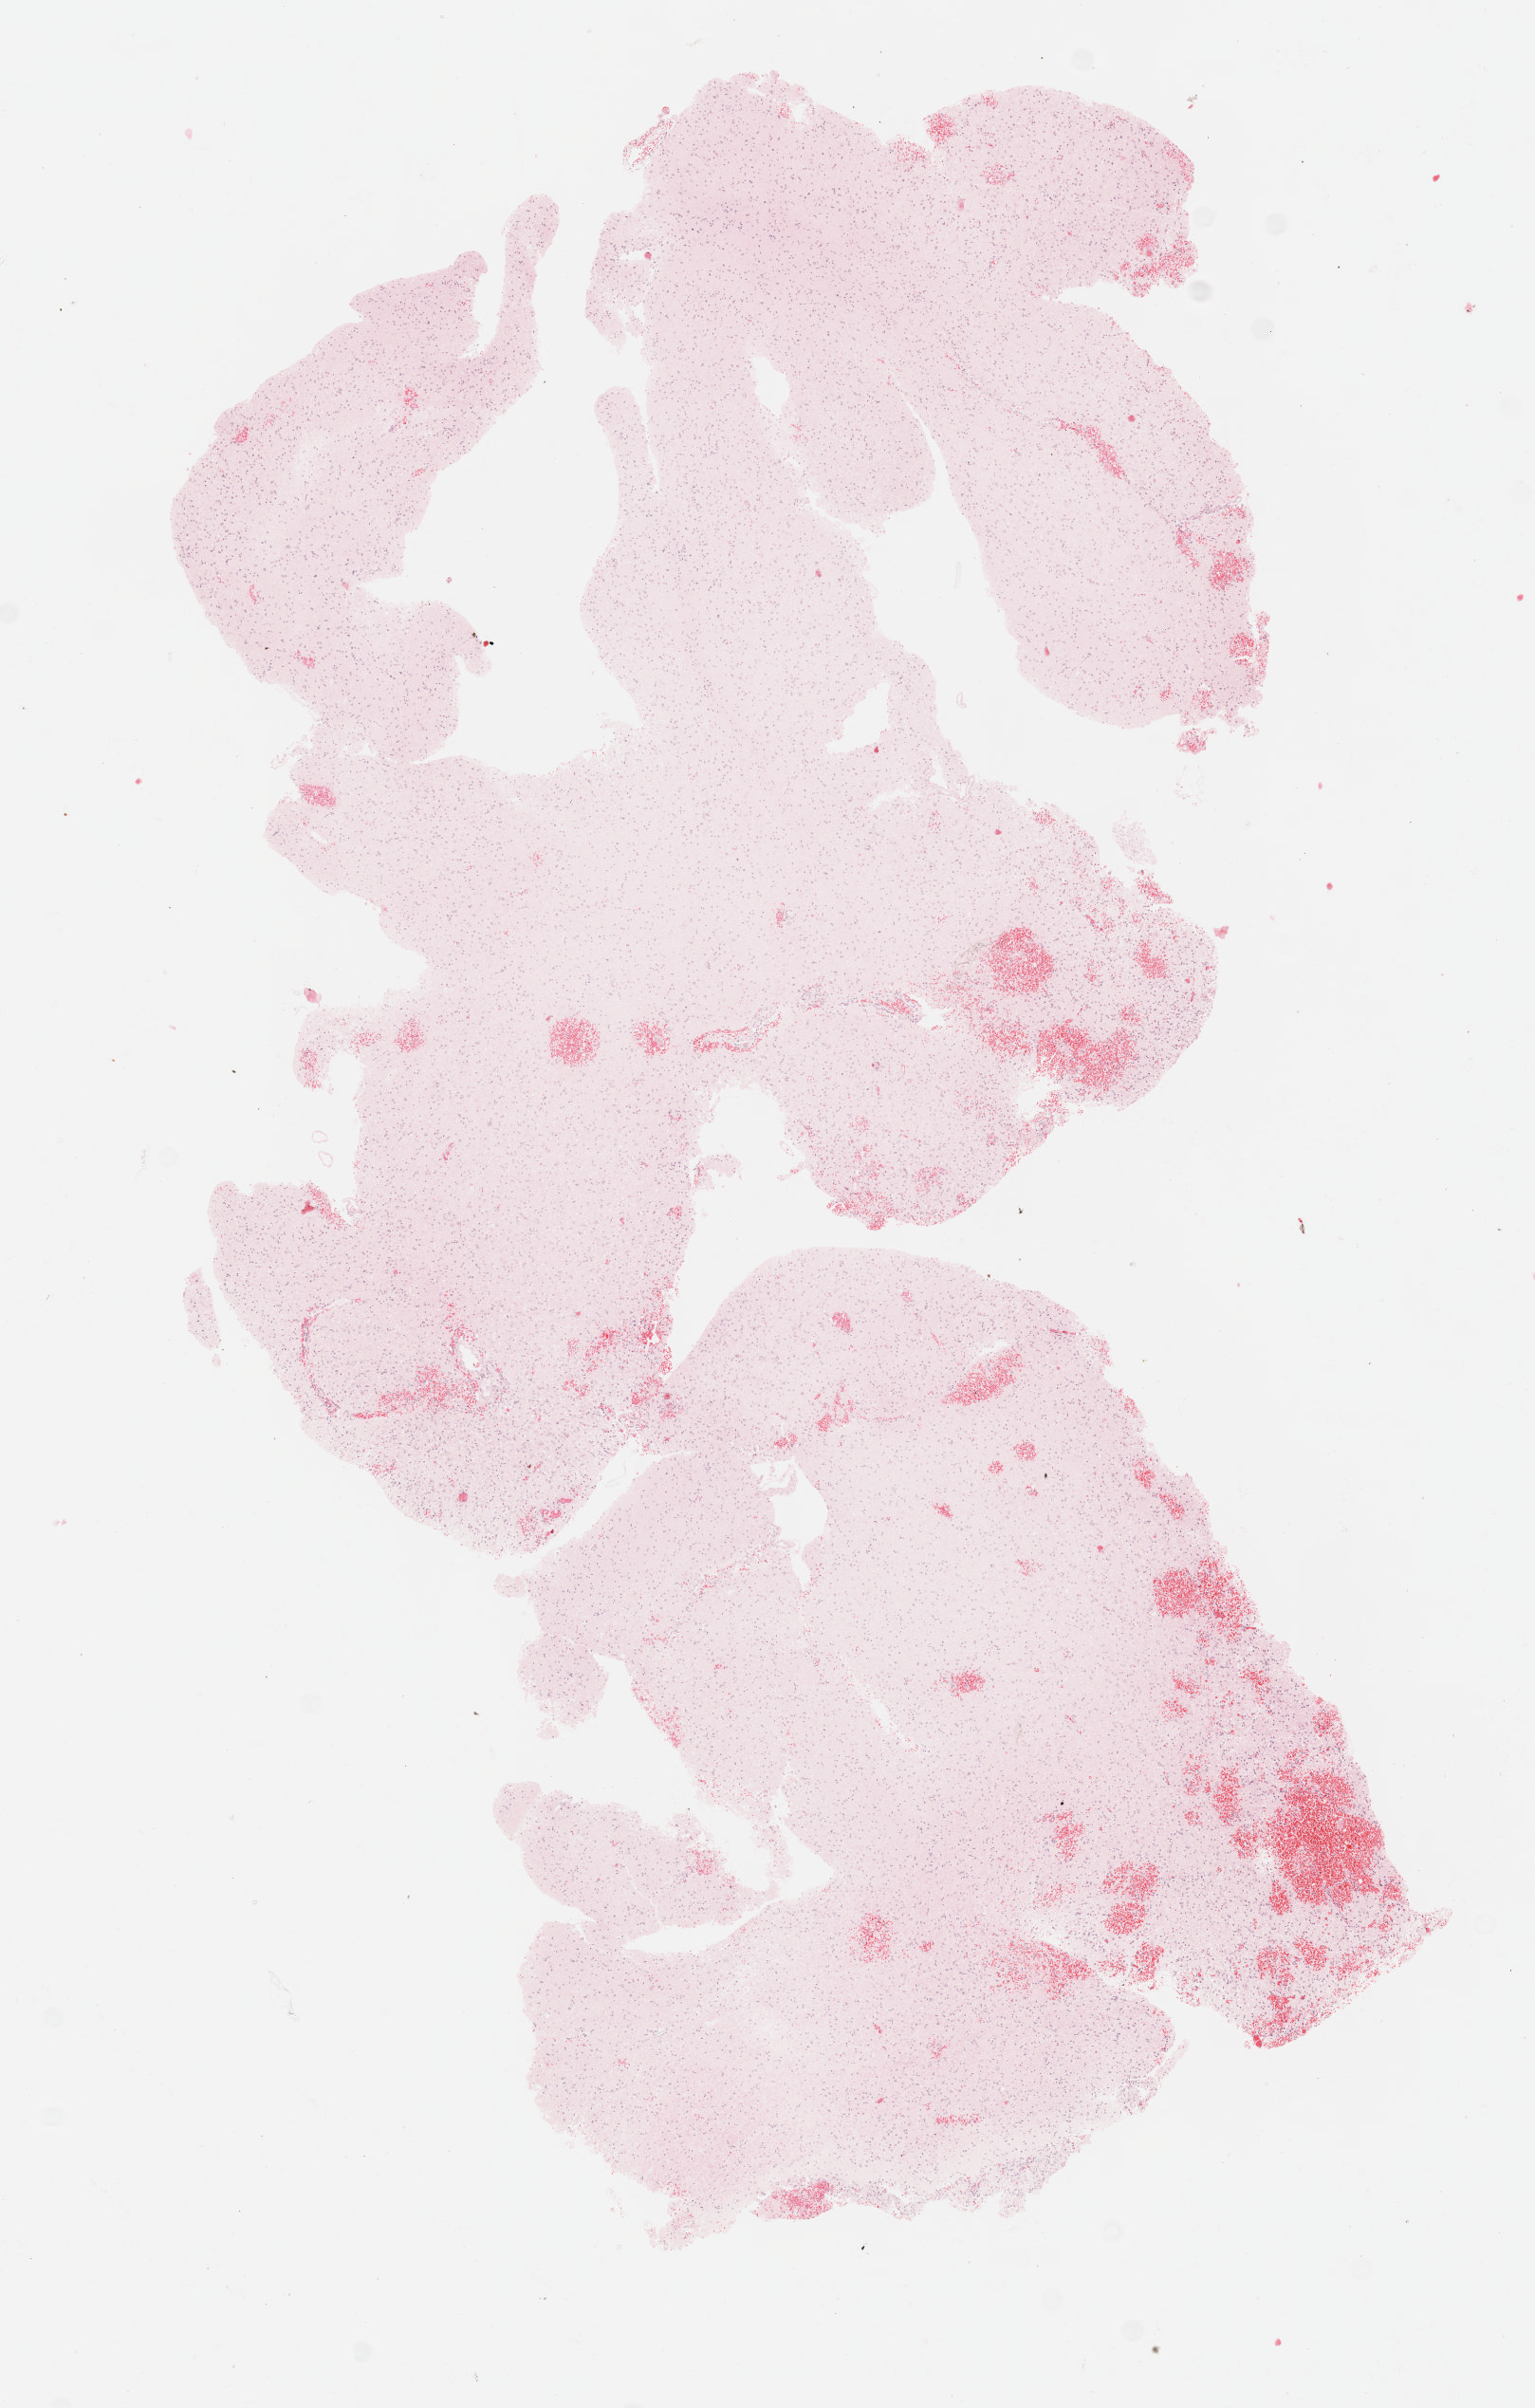
H&E-stained whole-slide image, low-resolution overview of the scanned area, about 6.5 x 10.3 mm (slide scanned at 40x), formalin-fixed paraffin-embedded (FFPE) diagnostic section, brain, primary tumour sample. Patient: male, age at initial diagnosis 66 years. Histologic grade: G3 (poorly differentiated).
Laterality: right. Pathologic diagnosis: Astrocytoma, anaplastic (cerebrum).